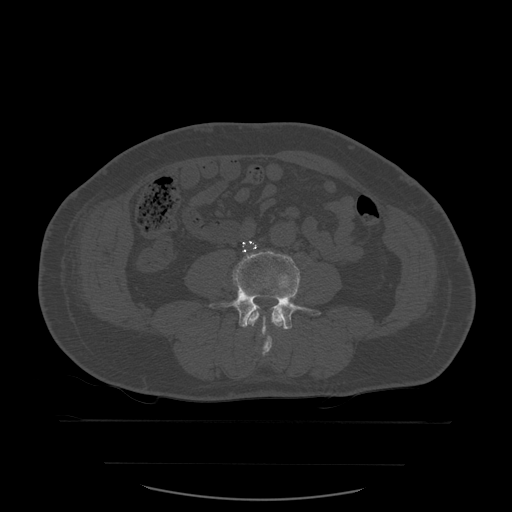
CT including the spine, one axial slice; slice 173 of 590 in the series (ordered by position); bone window (W 1800 / L 400 HU); 1.25 mm slice thickness; 512 × 512 image matrix, field of view 479 × 479 mm. Patient age 71 years. From the clinical record (not read from this slice): primary cancer: lung.
Structures marked on this image (semi-automatically segmented with operator editing):
- L3 vertebra: box from (x=245, y=311) to (x=284, y=356) px
- L4 vertebra: (x=209, y=251)–(x=312, y=335)